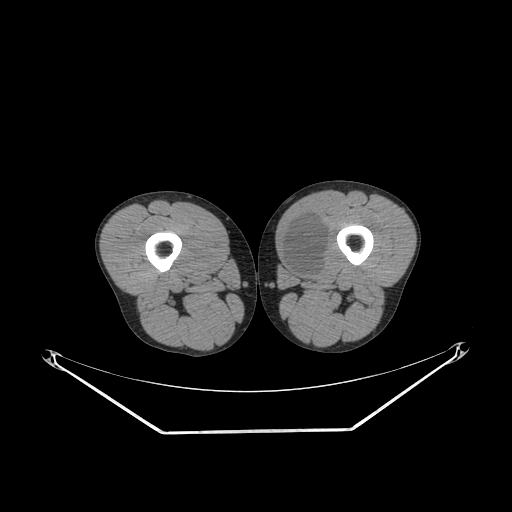
CT of an extremity soft-tissue mass (from a PET/CT study), one axial slice. Position 238 of 311 along the scan axis. Reconstruction kernel SOFT. 140 kVp. Soft-tissue window (W 400 / L 40 HU). 512 × 512 image matrix, field of view 500 × 500 mm. Male patient. From the clinical record (not read from this slice): histological type: mixoid liposarcoma; grade: low; site of the primary tumour: left thigh.
Annotated regions visible in this slice (expert contour drawn on MRI and transferred to this co-registered scan by the dataset authors):
- gross tumour volume (mass): bounding box (x1, y1, x2, y2) in pixels: (281, 215, 328, 277)